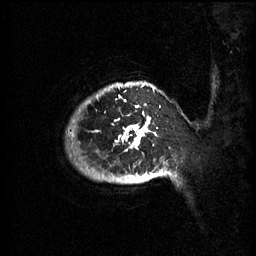
Breast MRI (dynamic contrast-enhanced), one sagittal slice. Slice 55 of 60 in the series (ordered by position). 3 images stored at this slice position (order not interpretable as contrast timing). 1.5 T. TE 4.2 ms, TR 11 ms. 2 mm slice thickness. 256 × 256 image matrix, field of view 220 × 220 mm. Female patient, age 51 years.
Annotated regions visible in this slice (semi-automatically segmented with operator editing):
- analysis volume of interest (the breast-tissue region the enhancement analysis was run in; not a lesion): box from (x=76, y=82) to (x=176, y=185) px
- tumour enhancement mask (voxels above the 70 % enhancement threshold inside the analysis volume of interest): (x=97, y=84)–(x=171, y=183)